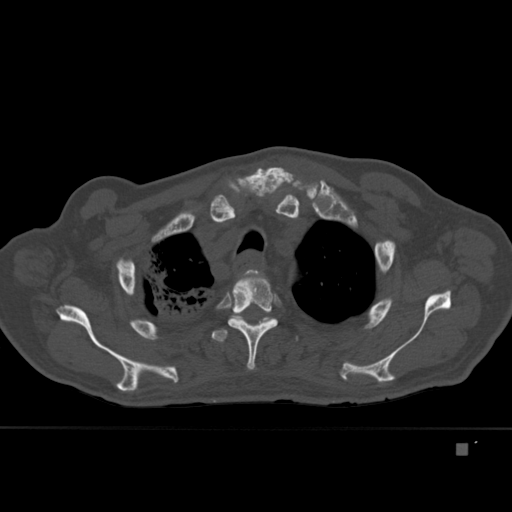
CT including the spine, one axial slice; position 333 of 451 along the scan axis; bone window (W 1800 / L 400 HU); 1.5 mm slice thickness; 512 × 512 image matrix, field of view 378 × 378 mm. Patient: male, 75 years. Case-level facts recorded for this patient, not image findings: primary cancer: prostate.
Outlined on this slice (semi-automatic segmentation, software-assisted and operator-edited):
- T2 vertebra: bounding box <242,269,268,281> (left, top, right, bottom; pixels)
- T3 vertebra: <224,274,278,370>
- T4 vertebra: <211,315,268,342>